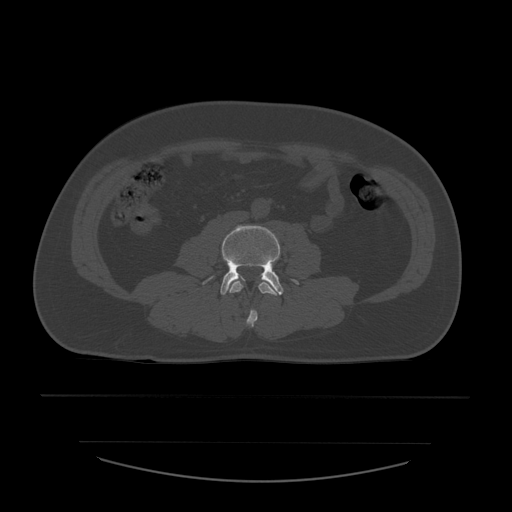
CT including the spine, one axial slice; slice 156 of 532 in the series (ordered by position); 120 kVp; bone window (W 1800 / L 400 HU); 1.25 mm slice thickness; 512 × 512 image matrix, field of view 441 × 441 mm. Patient age 44 years. Case-level facts recorded for this patient, not image findings: primary cancer: soft tissue sarcoma.
Structures marked on this image (semi-automatically segmented with operator editing):
- L3 vertebra: bounding box (x1, y1, x2, y2) in pixels: (229, 281, 278, 328)
- L4 vertebra: (203, 226, 299, 296)